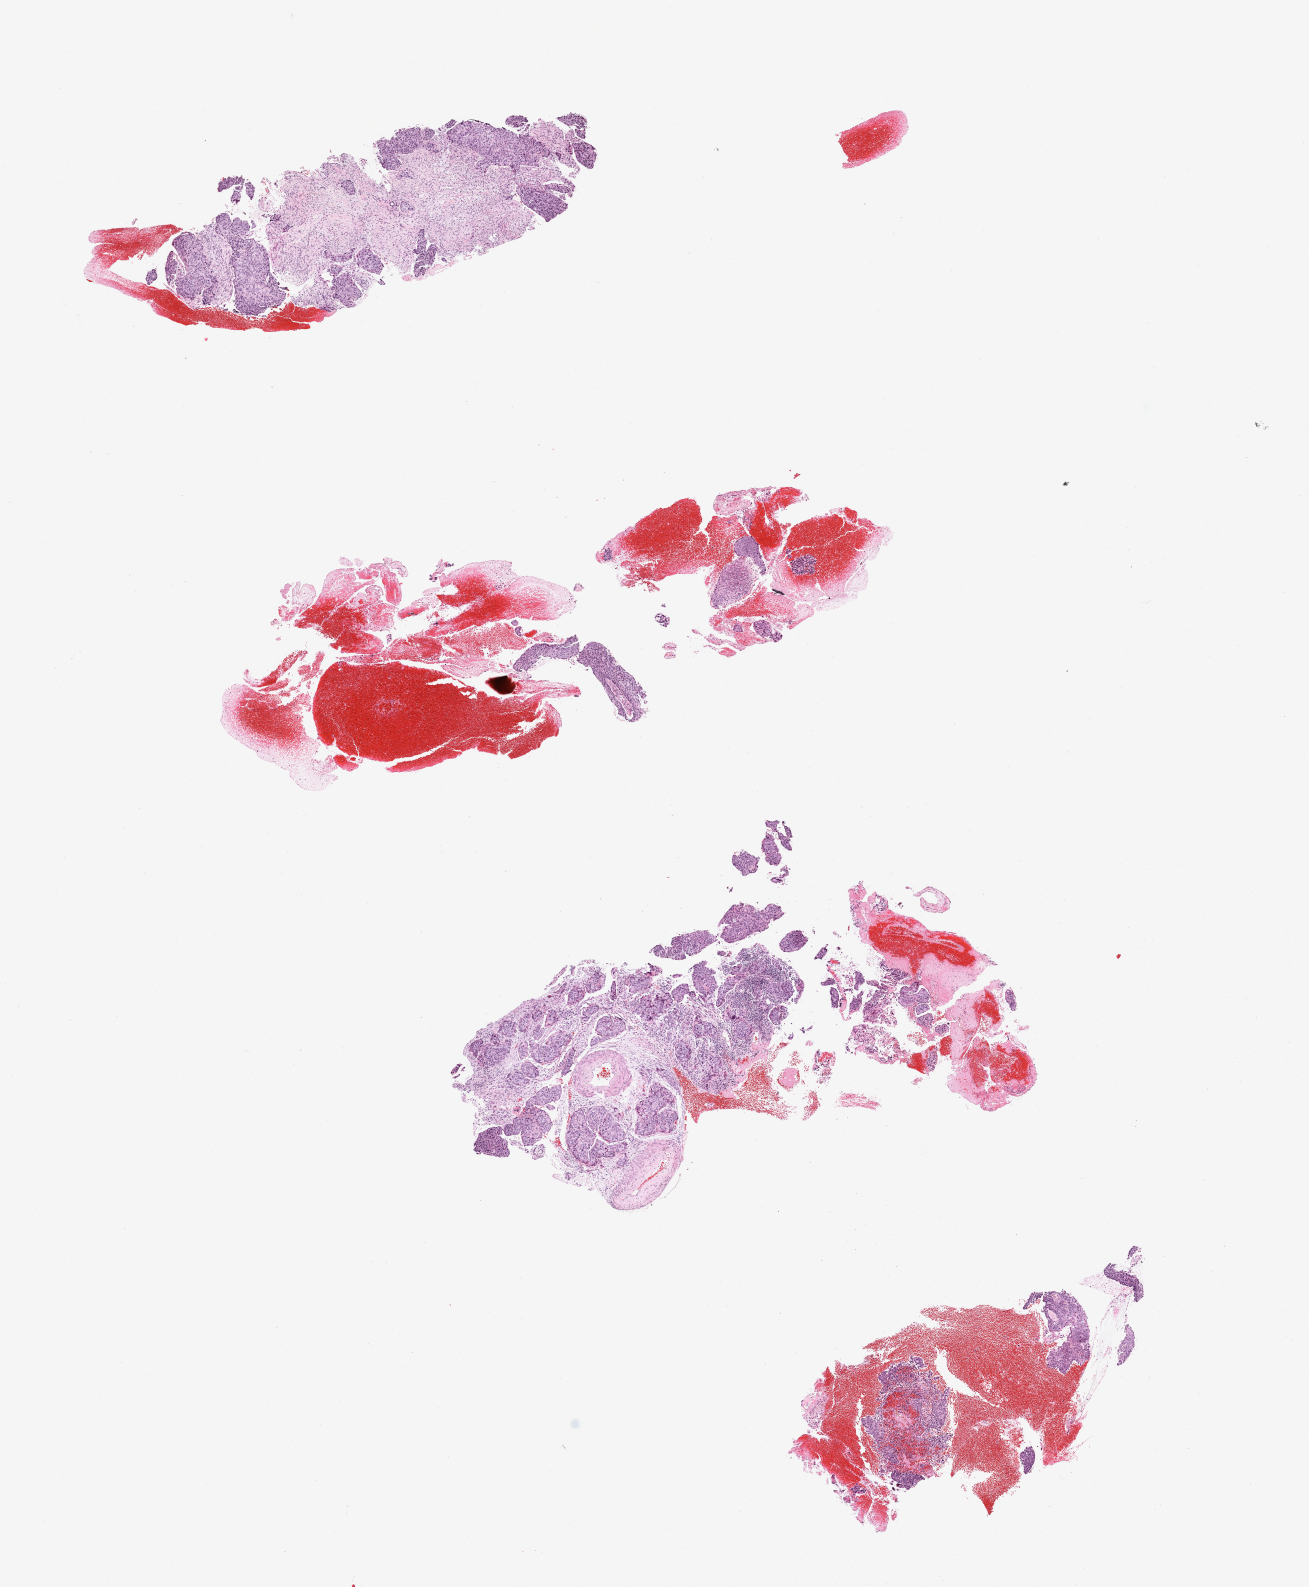
Whole-slide histology image, H&E-stained — a low-resolution overview of the entire scanned area, about 10.3 x 12.5 mm. Formalin-fixed paraffin-embedded (FFPE) diagnostic section. Primary tumour sample from the cervix. Patient: female, age at initial diagnosis 64 years.
Histologic diagnosis: Squamous cell carcinoma, NOS (cervix uteri).